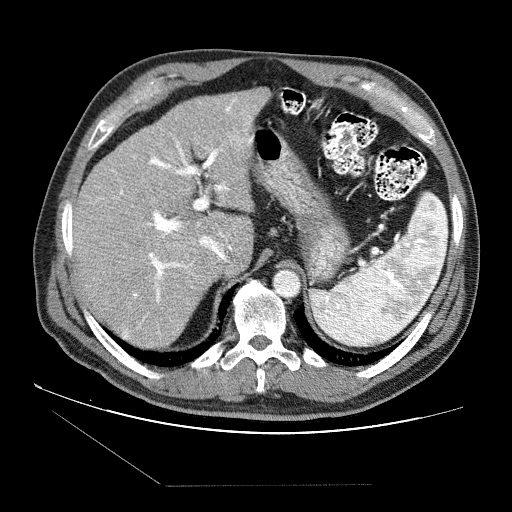
Contrast-enhanced abdominal CT (liver protocol), one axial slice. Slice 56 of 87 in the series (ordered by position). Reconstruction kernel STANDARD. 120 kVp. Soft-tissue window (W 400 / L 40 HU). 2.5 mm slice thickness. 512 × 512 image matrix, field of view 400 × 400 mm. Case-level facts recorded for this patient, not image findings: diagnosis: hepatocellular carcinoma (patient treated with transarterial chemoembolisation; whether this scan precedes or follows treatment is not stated here); TNM stage (as recorded): Stage-II; Child-Pugh class: B; tumour differentiation: no biopsy.
Outlined on this slice (semi-automatically segmented with operator editing):
- liver parenchyma outside the tumour (the mass and vessels are separate outlines, so this box may not span the whole liver): bounding box (x1, y1, x2, y2) in pixels: (72, 88, 270, 346)
- liver vessels: (100, 98, 253, 339)